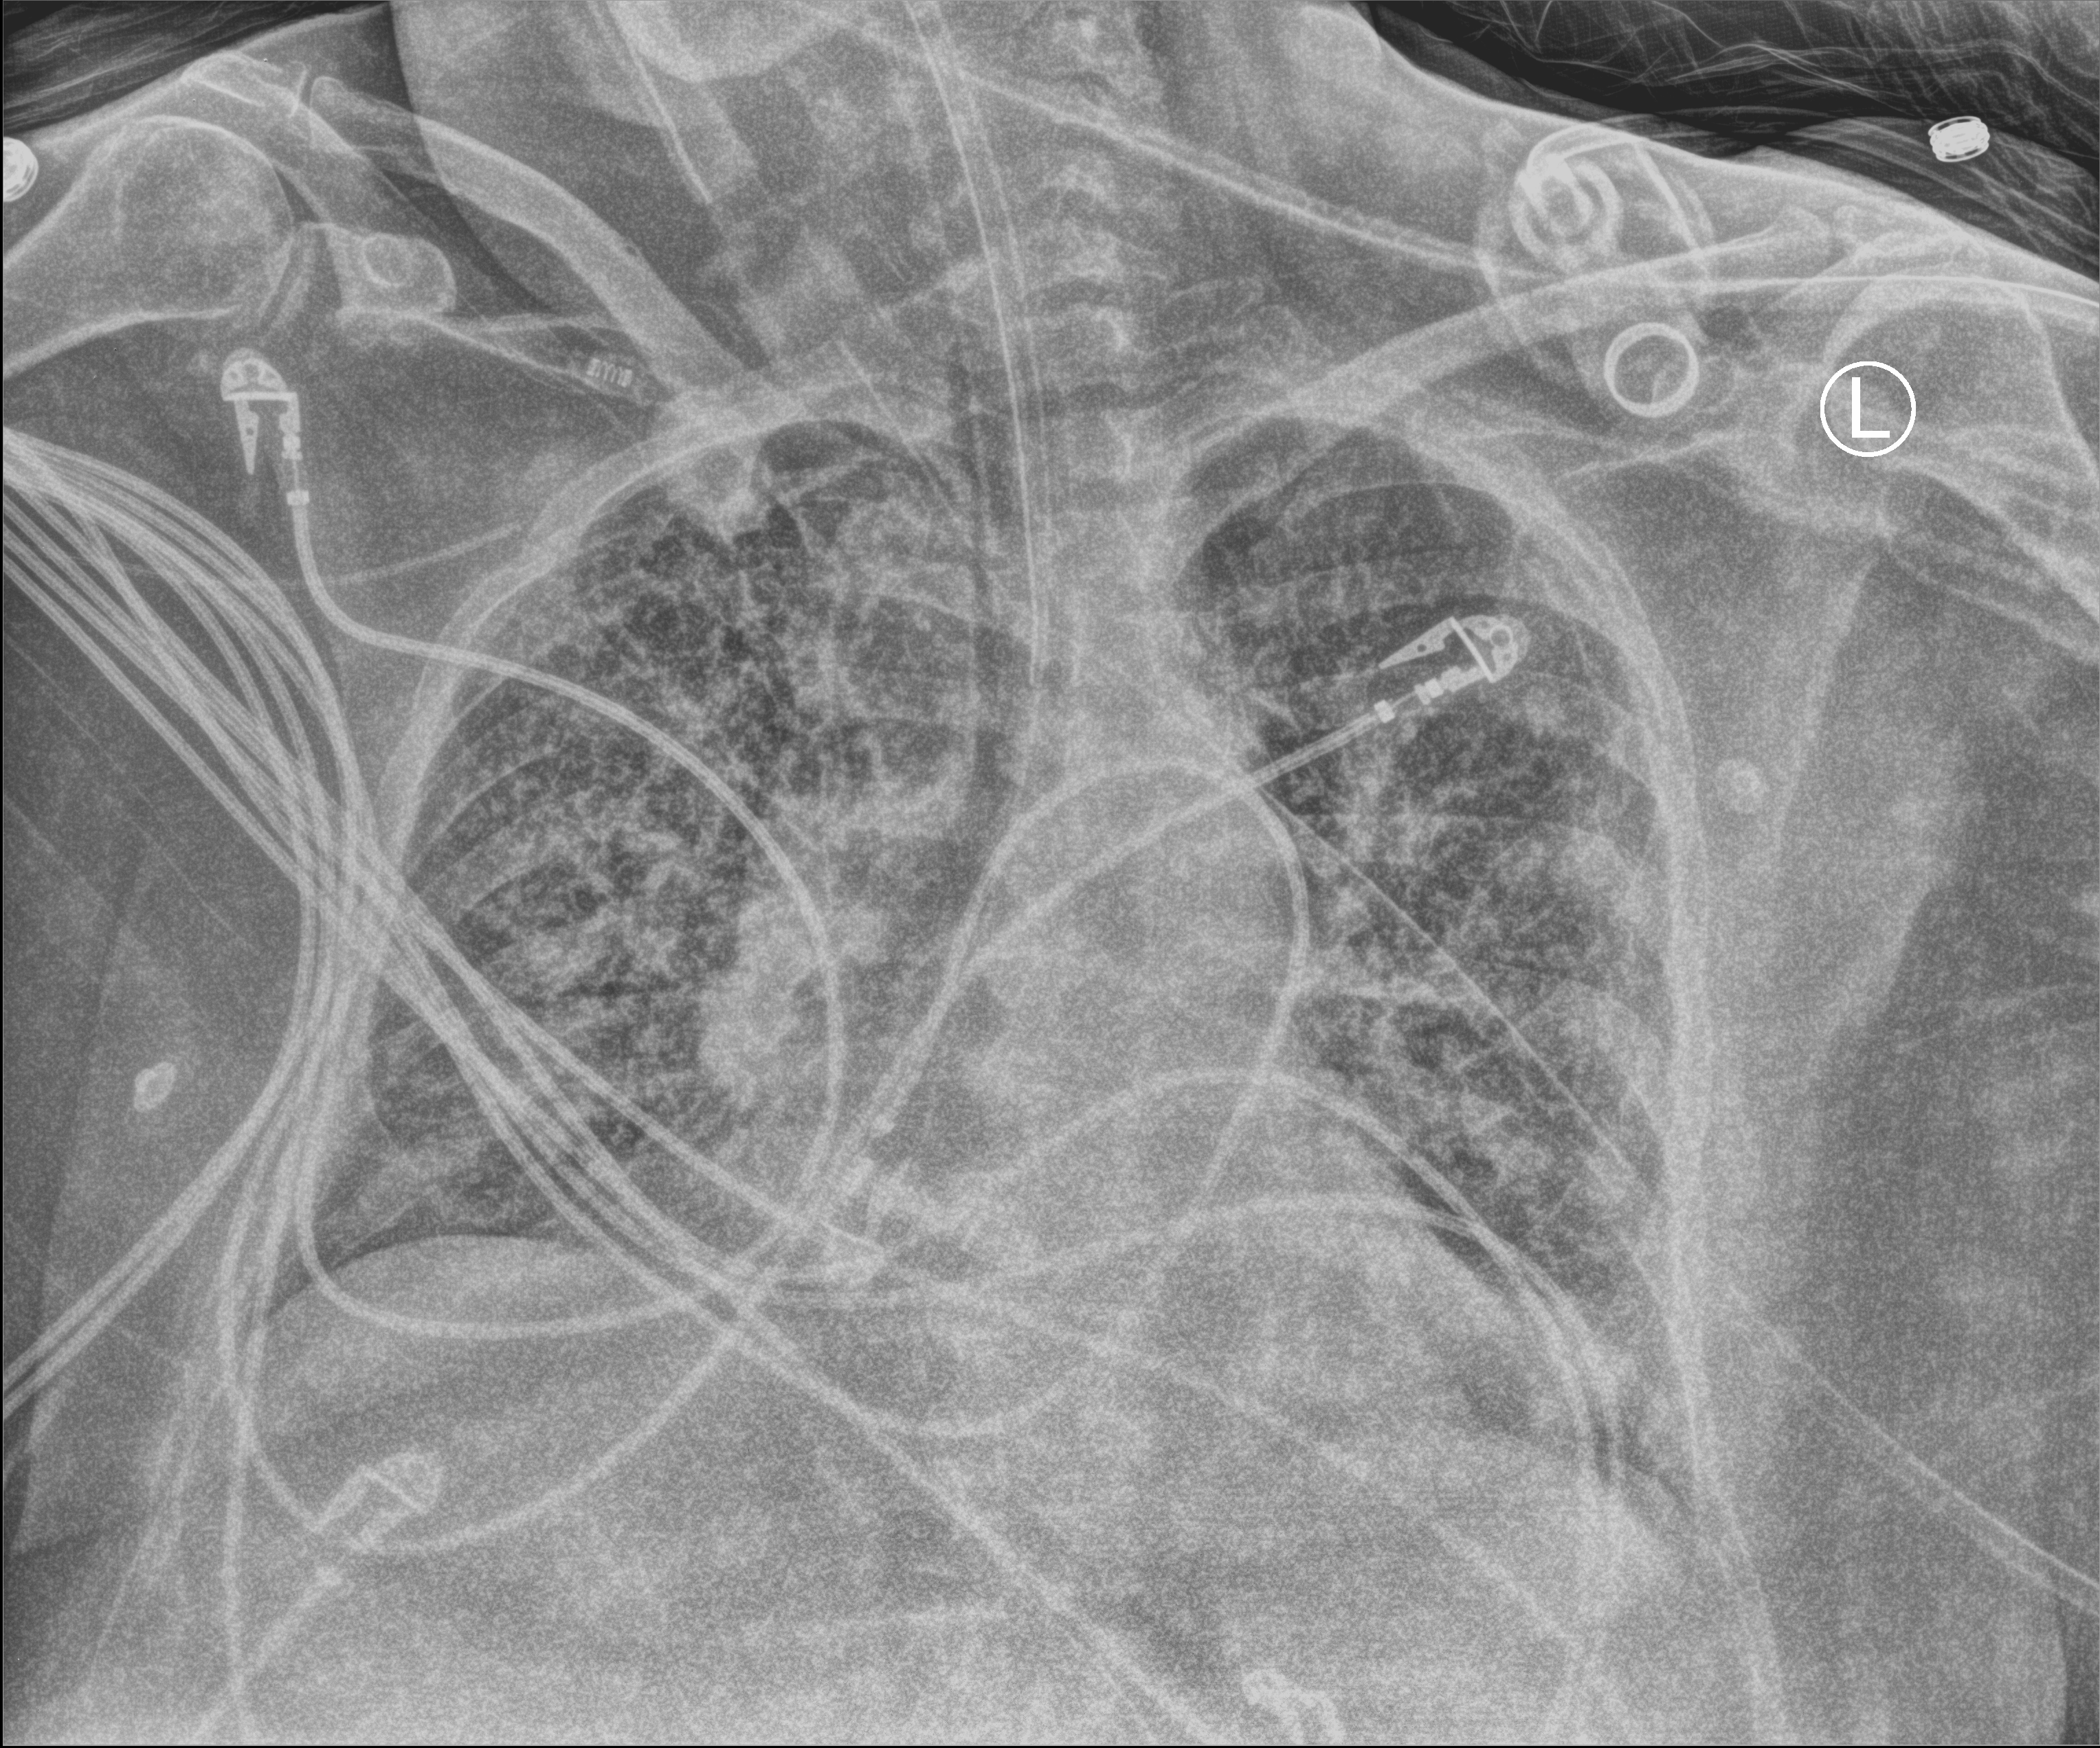
Bedside chest radiograph (computed radiography); anteroposterior (AP) projection. Female patient hospitalised with COVID-19, age 60–74 years.
From the hospital-stay record, not from the radiograph (when in the stay this image was taken is not recorded):
- diabetes (admission record): yes
- mechanically ventilated during this hospital stay: yes
- admitted to intensive care during this hospital stay: yes